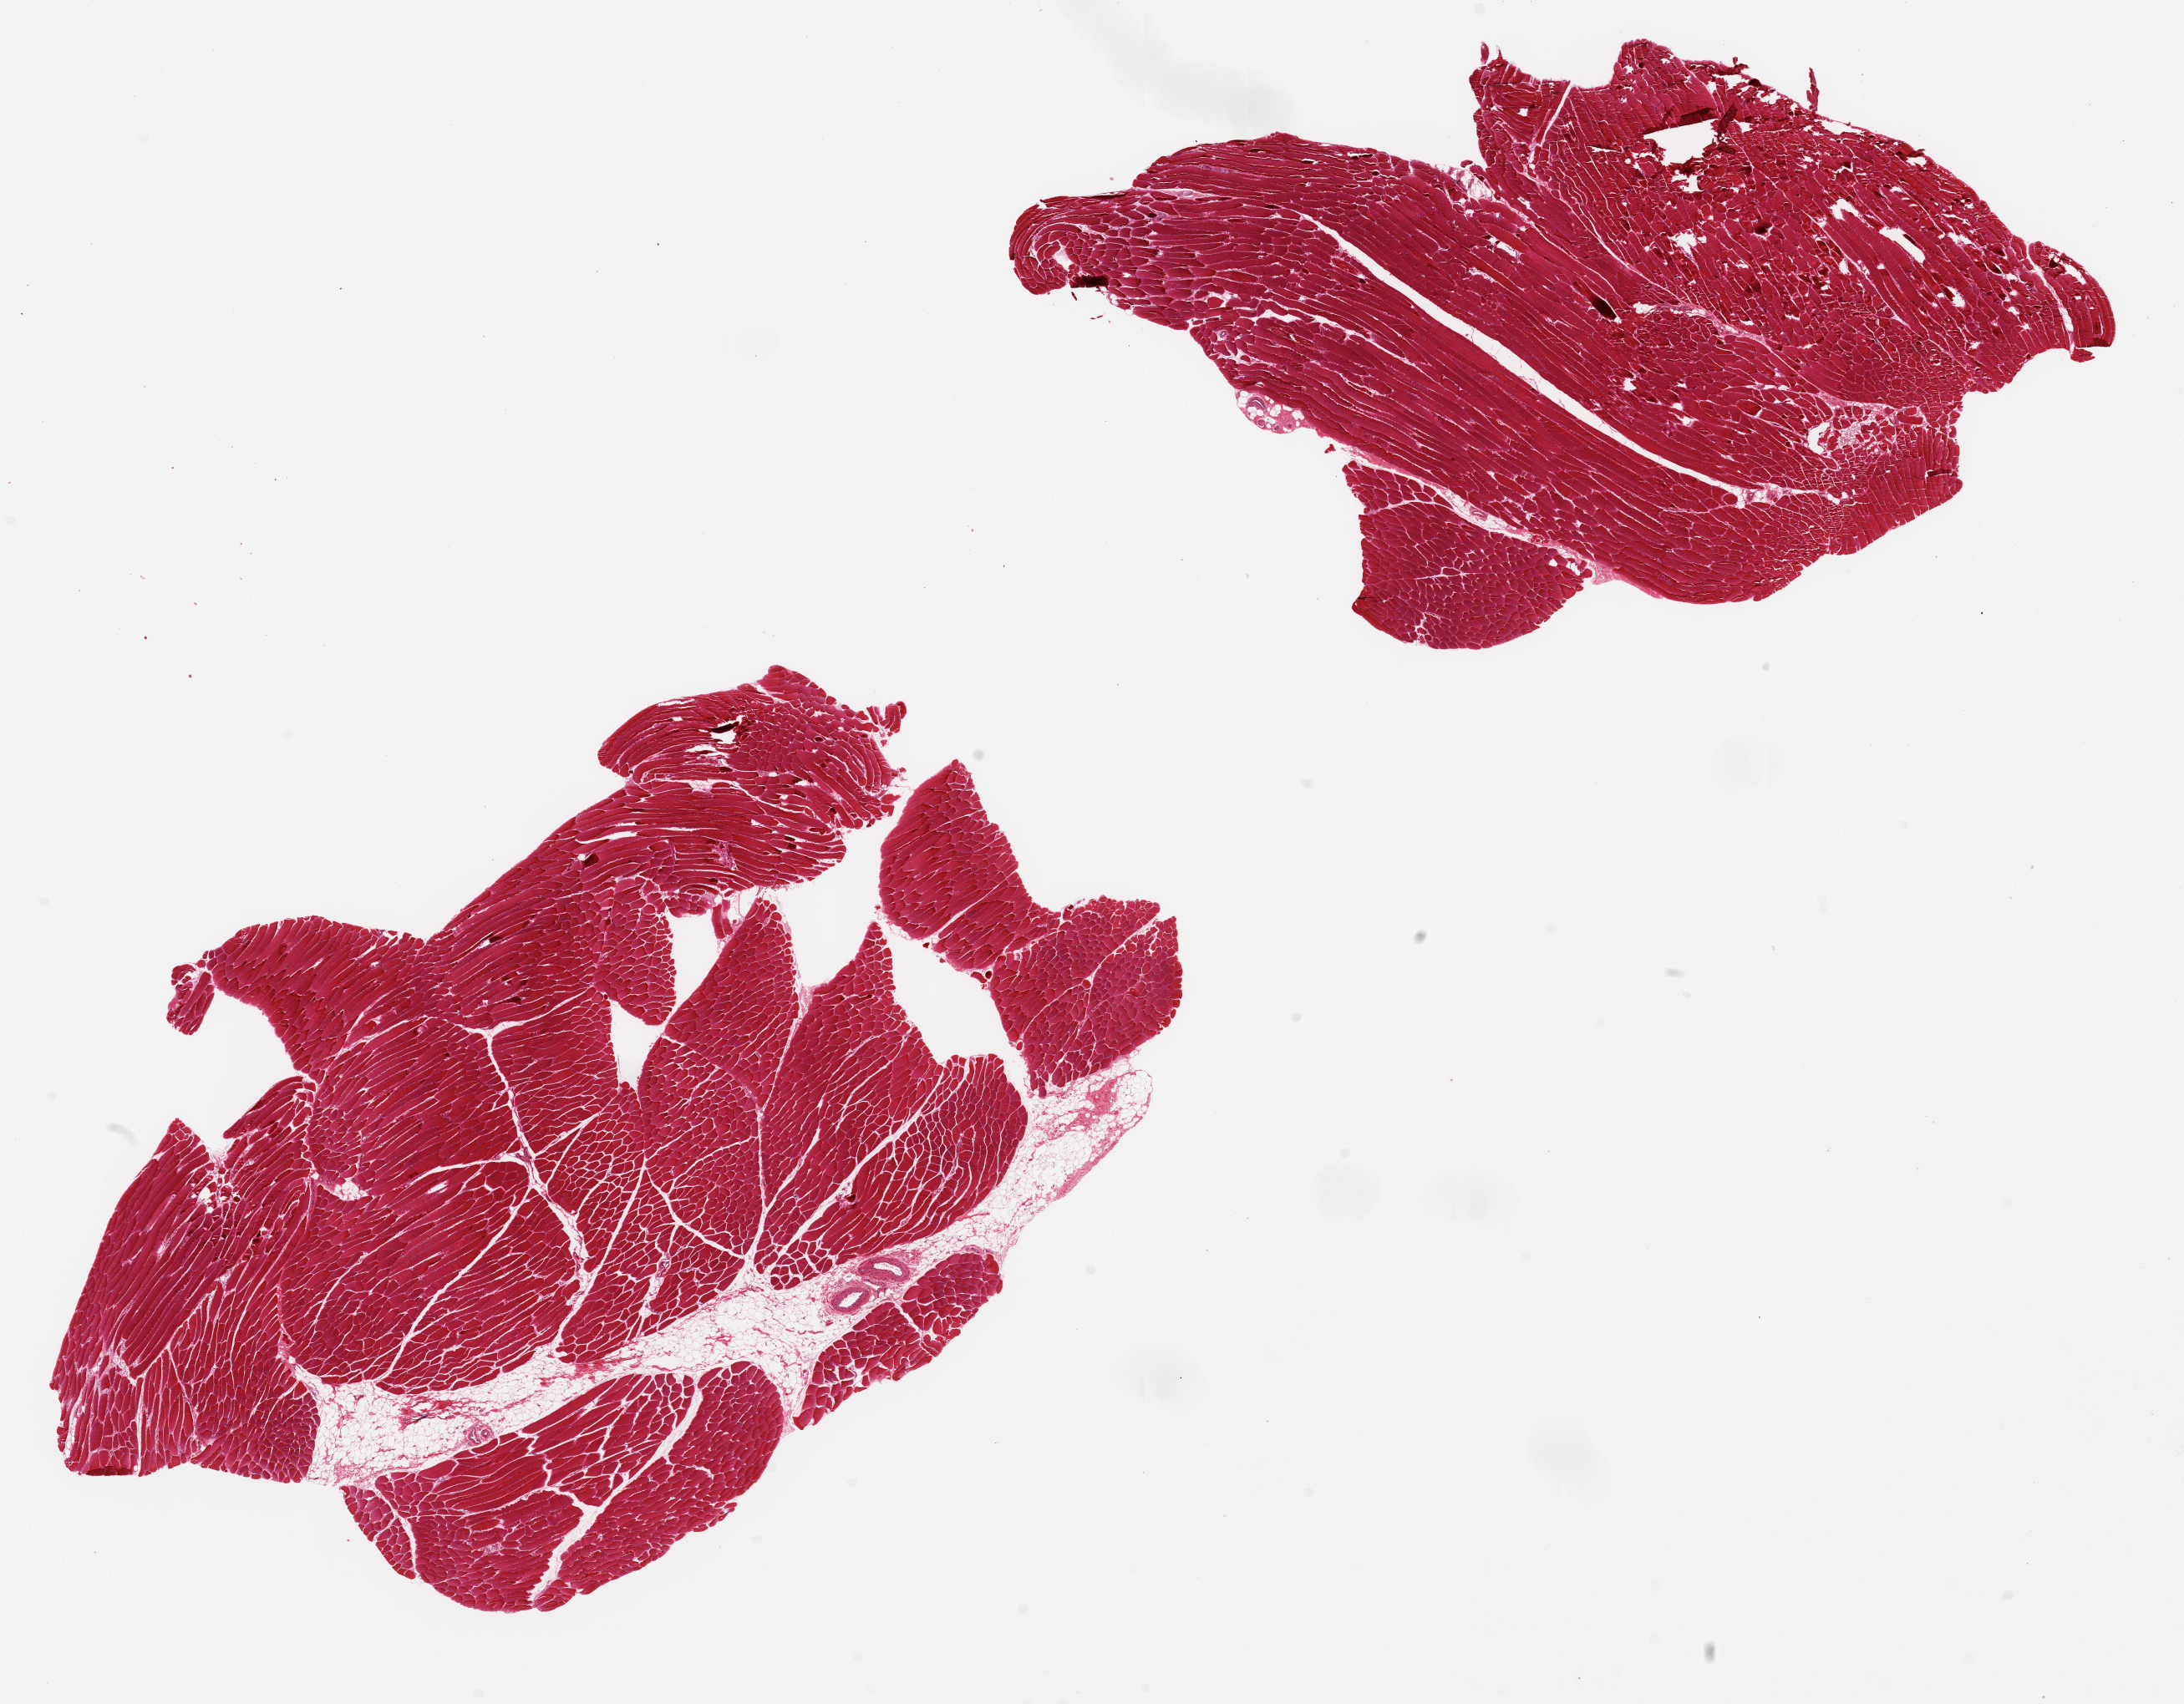
H&E whole-slide image, brightfield — whole scanned area (about 20.7 x 16.1 mm, acquisition: 20x scan) shown as a low-resolution overview; PAXgene-fixed, paraffin-embedded tissue; target tissue: skeletal muscle; donor tissue sample. Donor: male.
Reviewer comment on this tissue sample: 2 pieces 9x7 & 7x7 mm; larger has ~10% adipose between muscle bundles.